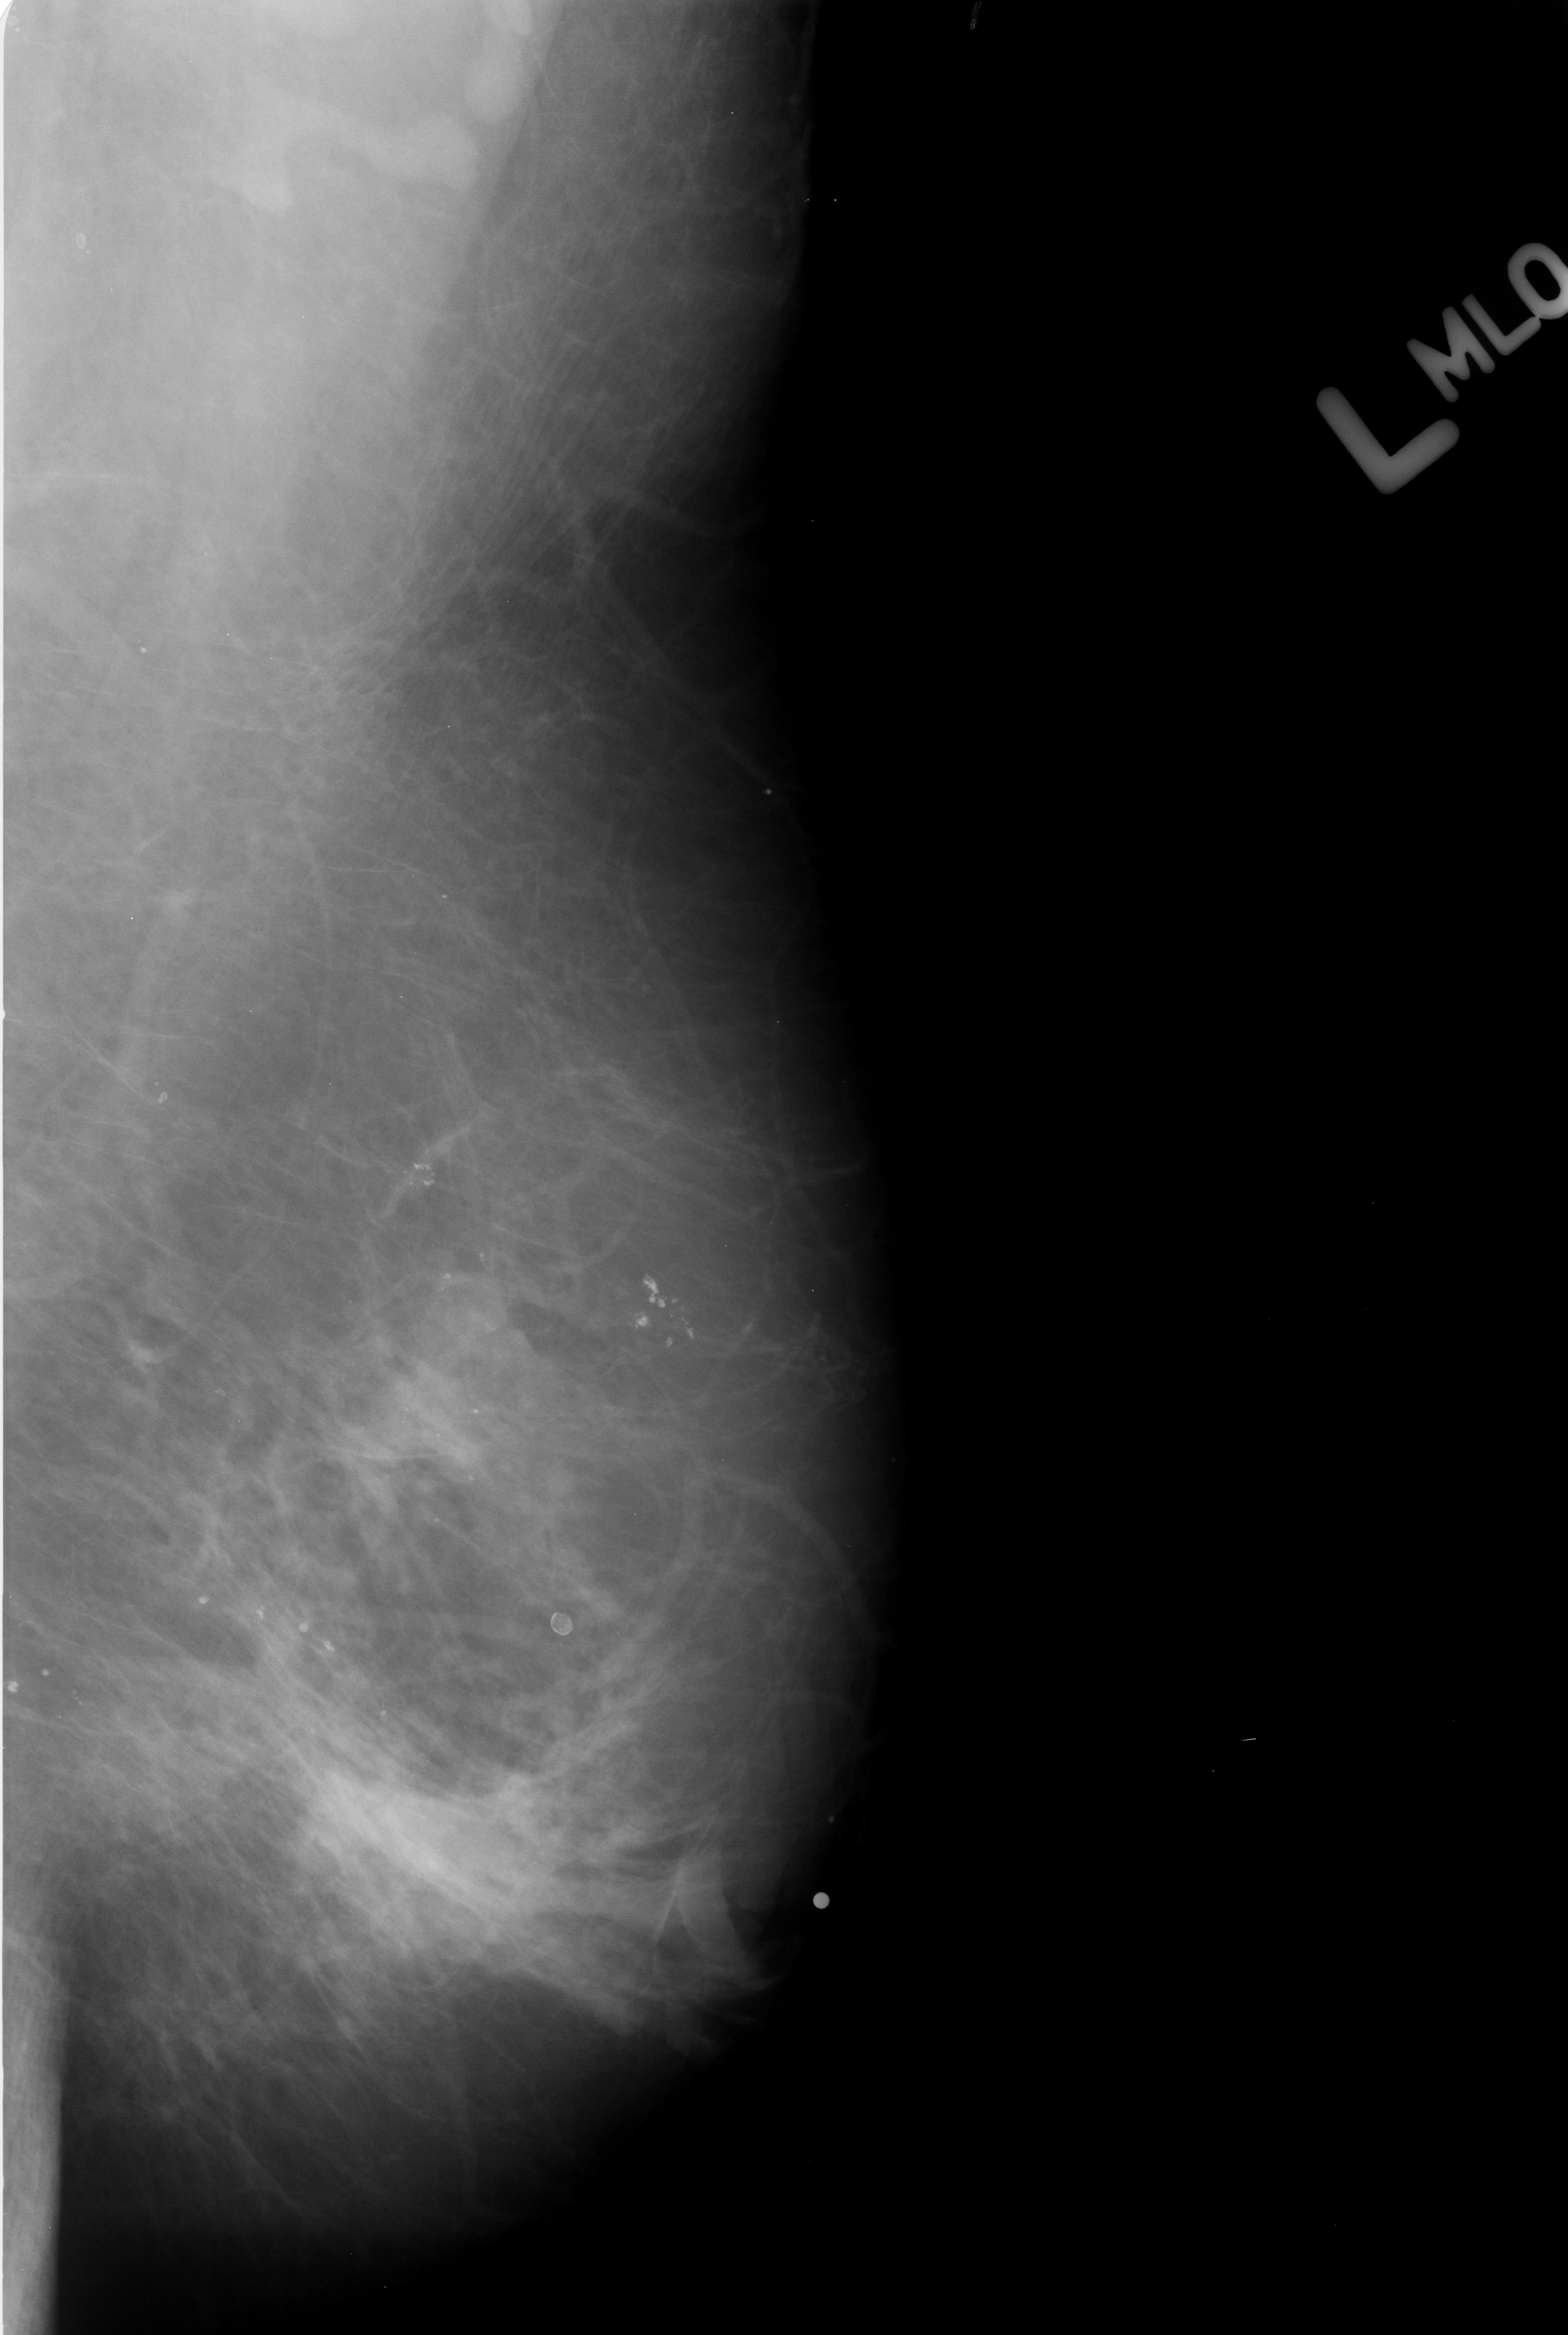
Digitized screen-film mammogram, left breast, mediolateral oblique (MLO) view, breast composition: scattered fibroglandular densities (BI-RADS density category 2 of 4).
- Calcifications, morphology pleomorphic, distribution clustered; BI-RADS assessment category 4; subtlety rating 3 on a 1 (subtle) to 5 (obvious) scale; pathology result (as recorded, not read from the image): benign.